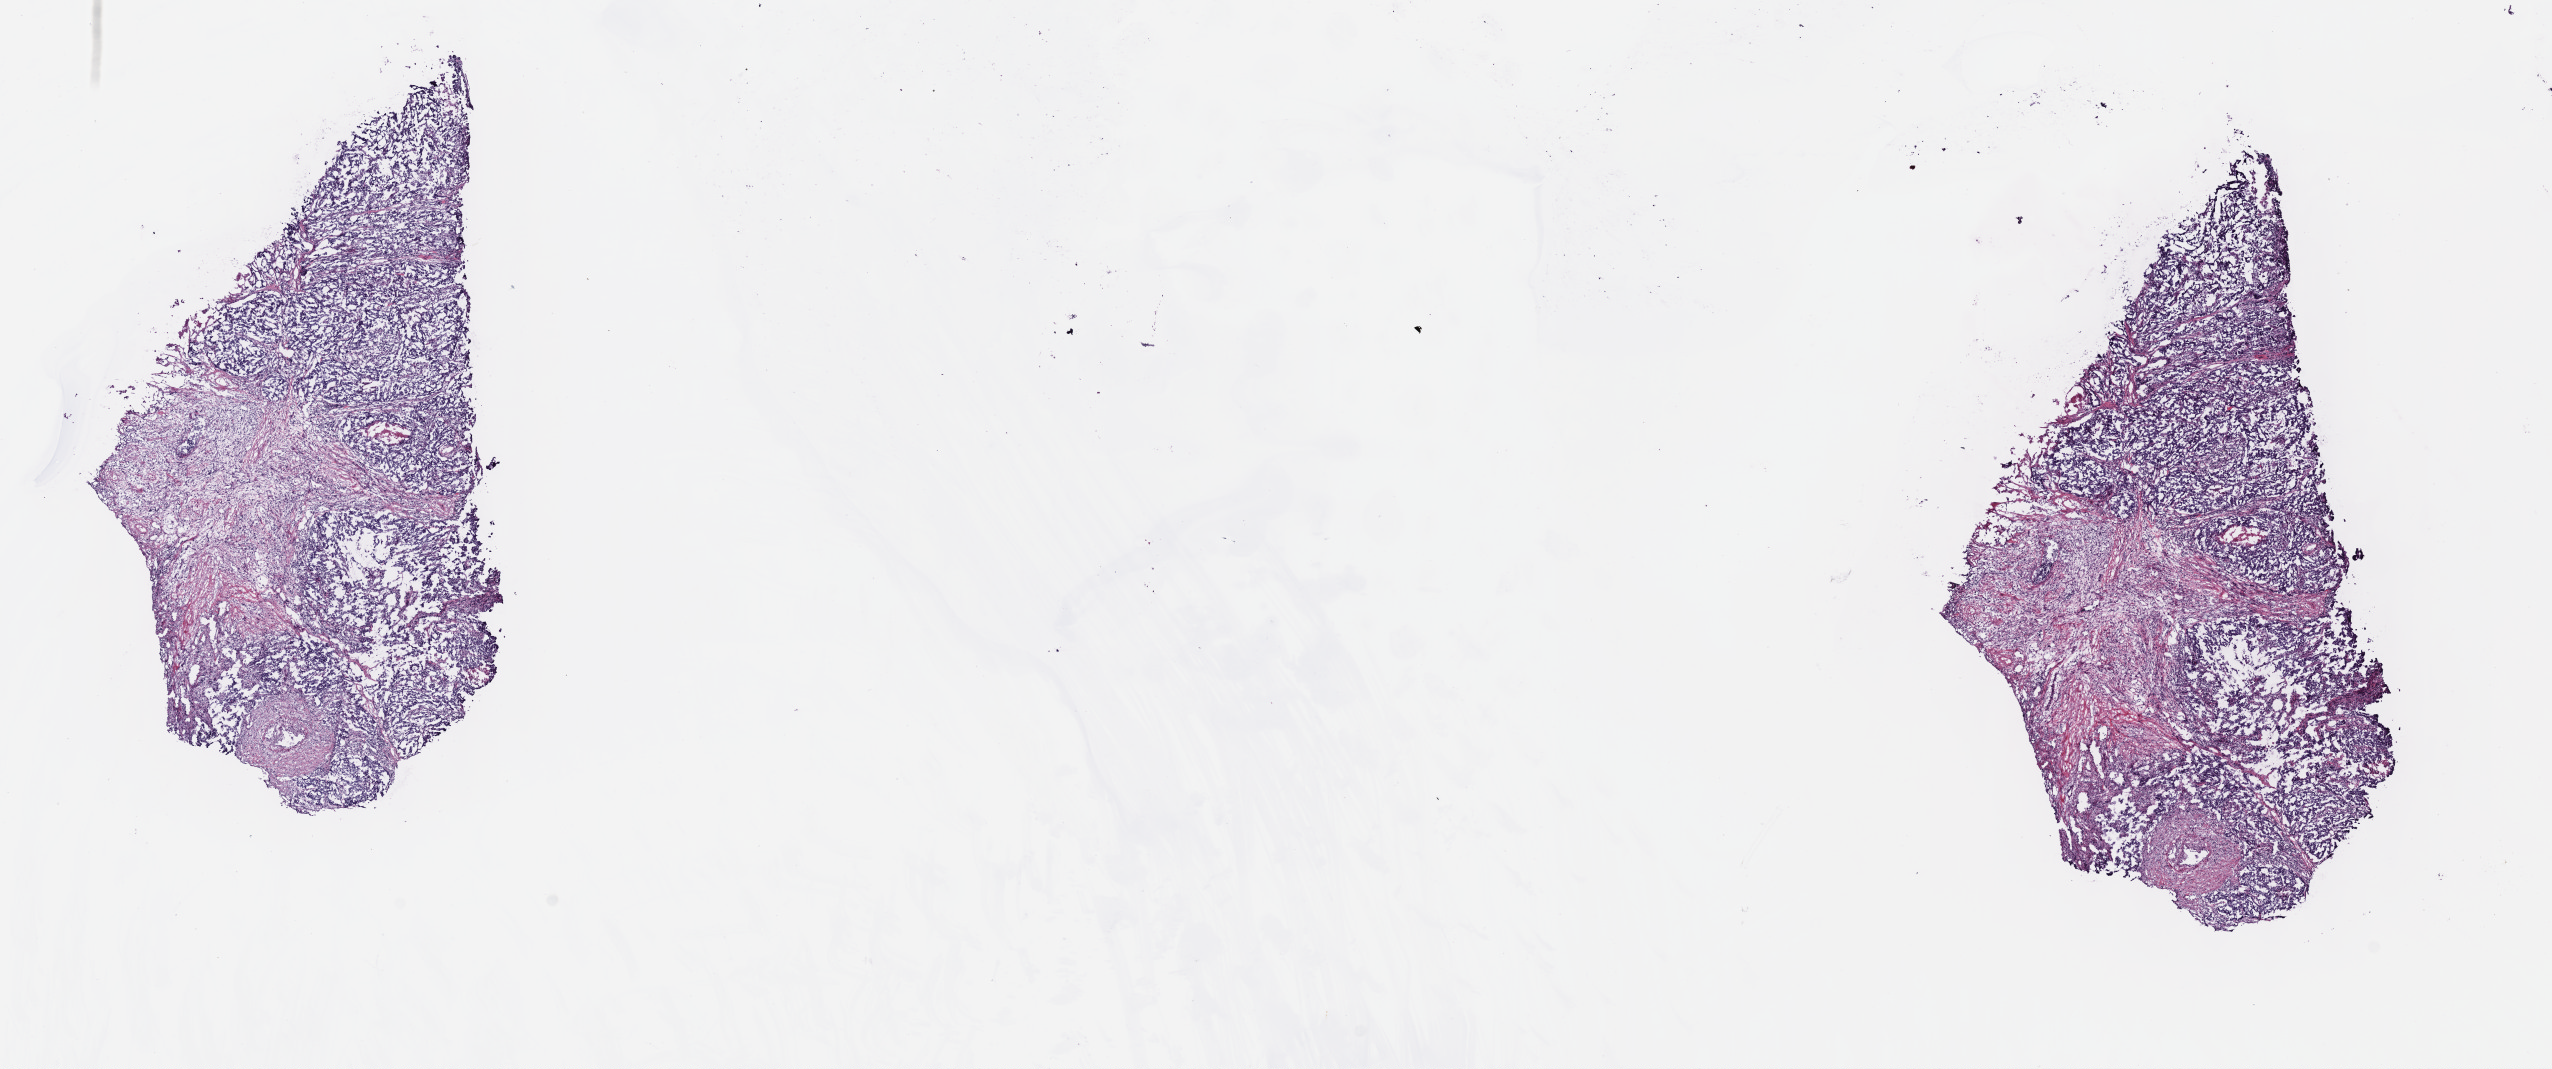
H&E whole-slide image, low-resolution overview of the scanned area, about 20.6 x 8.6 mm (slide scanned at 40x). Frozen section from the top of the tissue portion. Primary tumour sample from the testis. Patient: male, age at initial diagnosis 36 years. Composition of this section per pathologist review: tumour cells 55%, tumour nuclei 60%, normal cells 0%, stromal cells 40%, necrosis 5%. Inflammatory infiltration, as recorded: lymphocyte infiltration 0%, monocyte infiltration 0%, neutrophil infiltration 0%.
Diagnosis: Embryonal carcinoma, NOS. Laterality: left. AJCC pathologic stage: IB (7th edition).